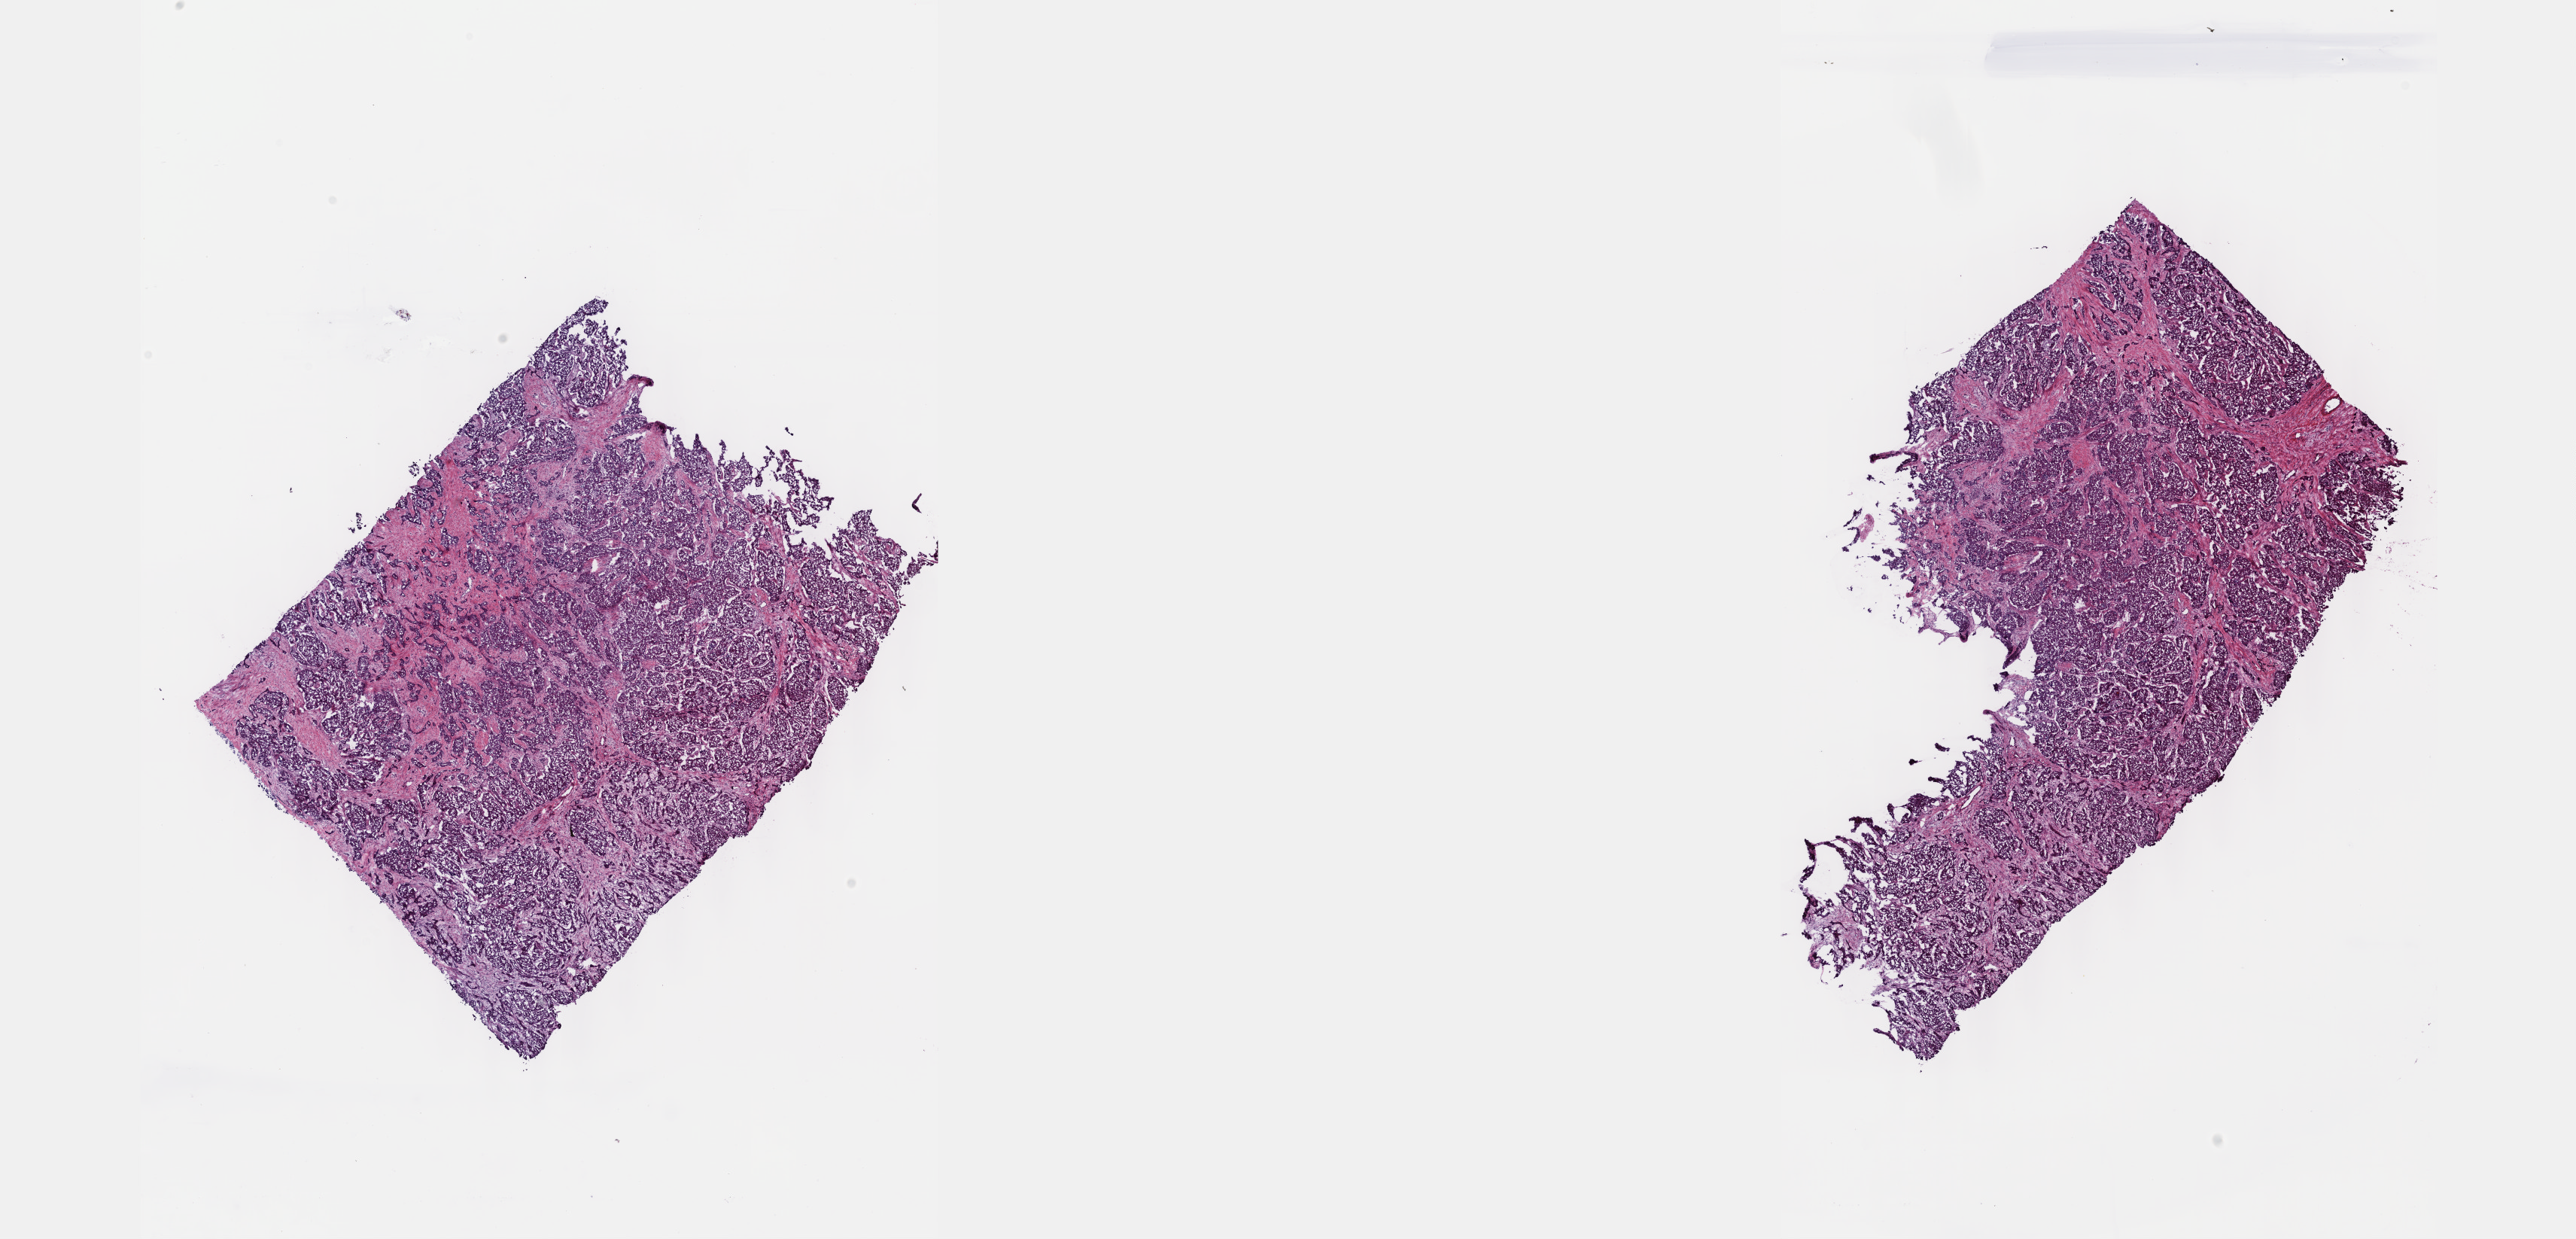
Whole-slide histology image, H&E-stained, low-resolution overview of the scanned area, about 27.7 x 13.3 mm (slide scanned at 40x), frozen section from the top of the tissue portion, sample: primary tumour, bile duct. Patient: female, age at initial diagnosis 51 years. Pathologist review of this section (percent, as recorded): tumour cells 70%, tumour nuclei 80%.
Histologic diagnosis: Cholangiocarcinoma (intrahepatic bile duct).